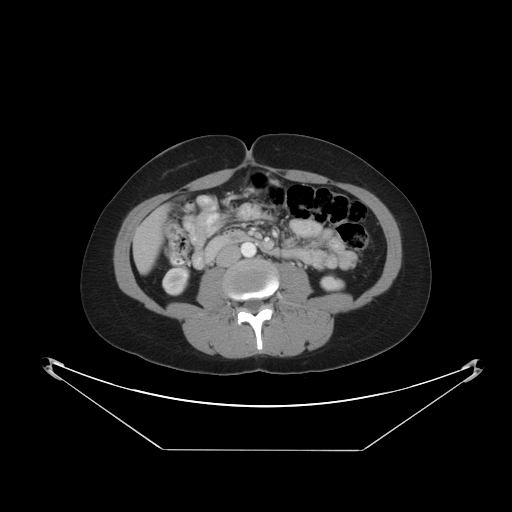
Contrast-enhanced abdominal CT, one axial slice. Slice 11 of 48 in the series (ordered by position). Reconstruction kernel STANDARD. 120 kVp. Intravenous contrast given. Soft-tissue window (W 400 / L 40 HU). 512 × 512 image matrix, field of view 482 × 482 mm. Female patient, age 38 years. Case-level facts recorded for this patient, not image findings: diagnosis: colorectal cancer liver metastases, imaged before liver resection; multiple liver metastases: yes; largest metastasis: 2.5 cm.
Structures marked on this image (expert manual segmentation):
- liver: box from (x=133, y=207) to (x=168, y=273) px